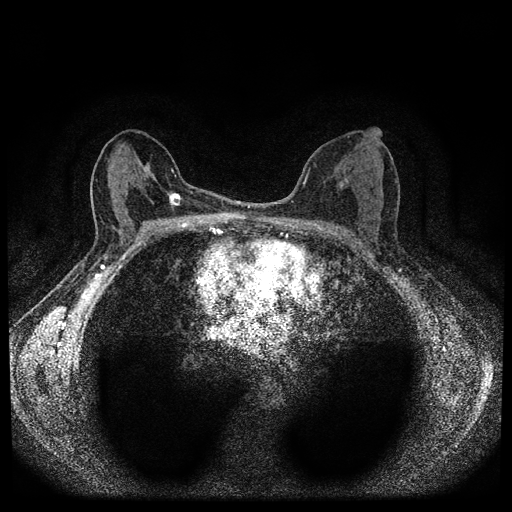
Breast MRI (dynamic contrast-enhanced, multi-phase), one axial slice. Slice 51 of 112 in the series (ordered by position). Dynamic contrast-enhanced series, time point 2 of 5 at this slice position (early post-contrast). 1.5 T. TE 2.7 ms, TR 5.4 ms. 2 mm slice thickness. 512 × 512 image matrix, field of view 320 × 320 mm. Patient: female, 61 years.
Outlined on this slice (semi-automatic segmentation, software-assisted and operator-edited):
- breast lesion (labelled benign in the annotation): bounding box (x1, y1, x2, y2) in pixels: (337, 179, 348, 190)
- breast lesion (labelled 'tumour' in the annotation; benign lesions carry a separate 'benign' label): (168, 192, 181, 207)